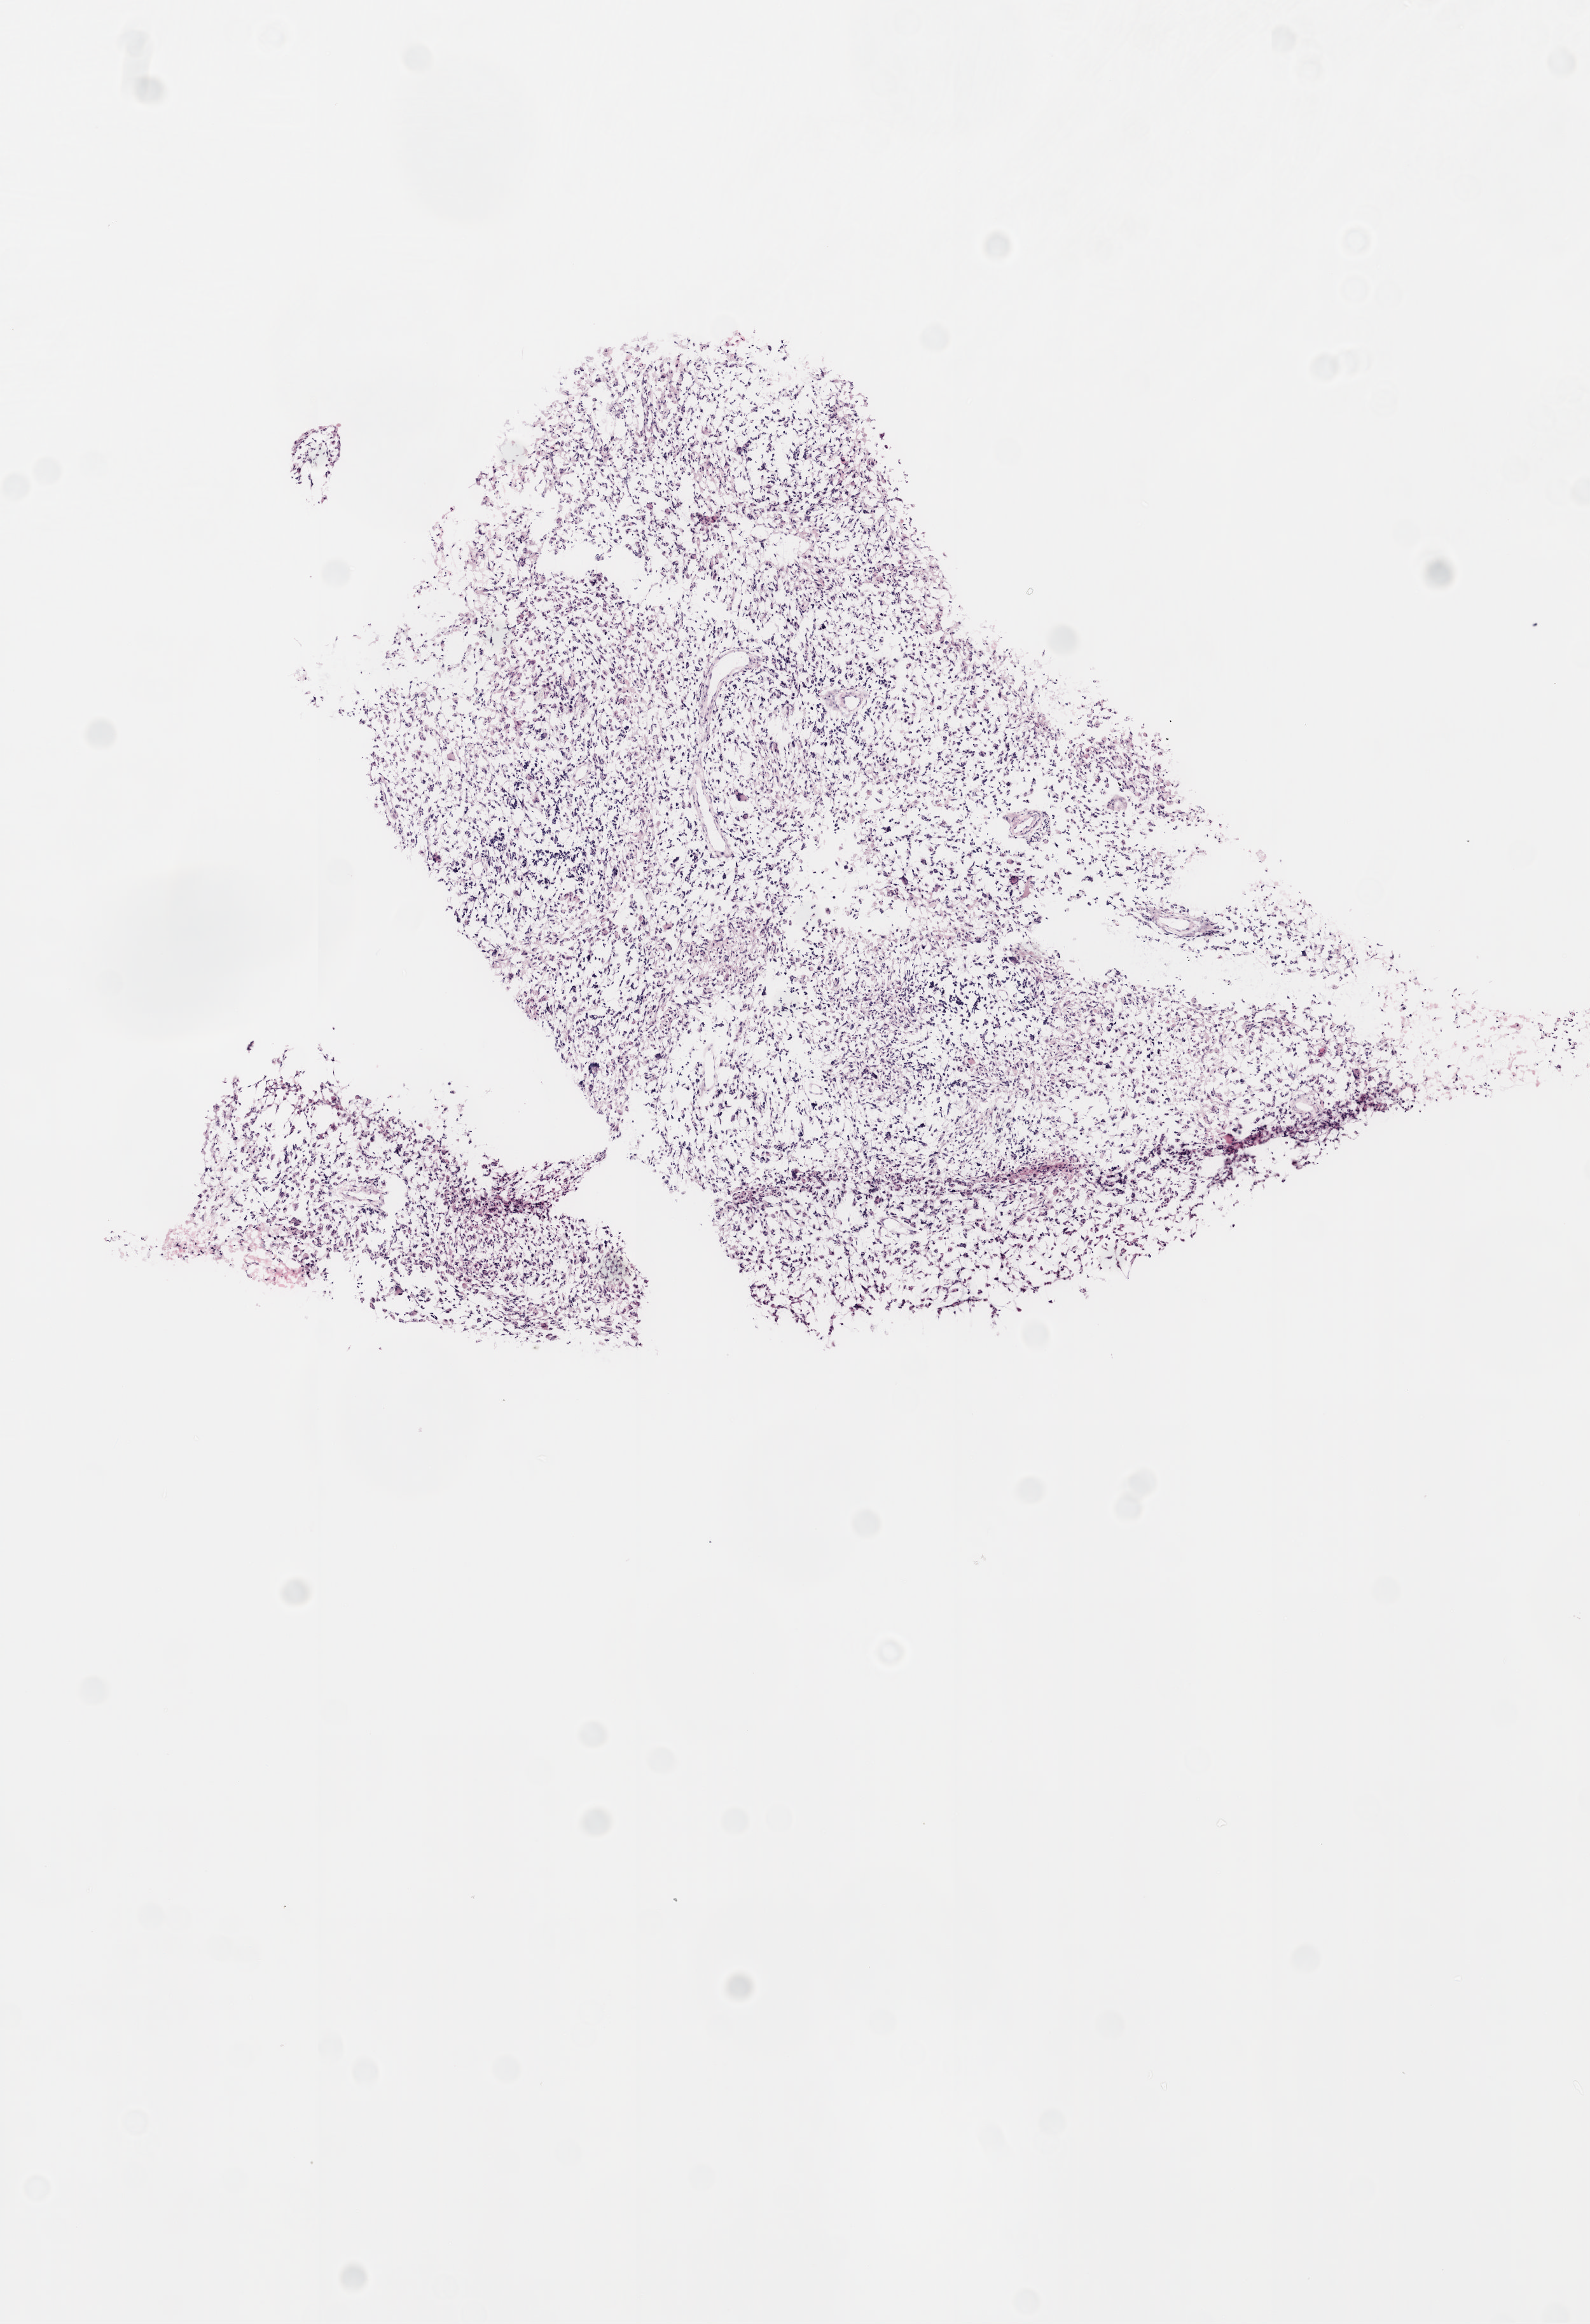
Whole-slide histology image, H&E-stained, whole scanned area (about 5.0 x 7.3 mm, acquisition: 20x scan) shown as a low-resolution overview. Frozen section from the top of the tissue portion. Primary tumour sample from the brain. Patient: female, age at initial diagnosis 72 years. Pathologist review of this section (percent, as recorded): tumour cells 100%, tumour nuclei 90%, normal cells 0%, stromal cells 0%, necrosis 0%.
- pathologic diagnosis: Glioblastoma